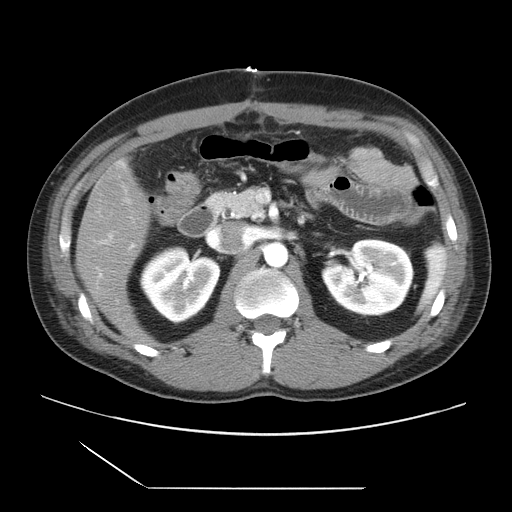
Contrast-enhanced abdominal CT, one axial slice; position 9 of 39 along the scan axis; intravenous contrast given; soft-tissue window (W 400 / L 40 HU); 5 mm slice thickness; 512 × 512 image matrix, field of view 395 × 395 mm. Male patient, age 39 years. From the clinical record (not read from this slice): diagnosis: colorectal cancer liver metastases, imaged before liver resection; multiple liver metastases: yes; largest metastasis: 1.3 cm.
Structures marked on this image (outlined manually by an expert reader):
- hepatic veins: bounding box [x1, y1, x2, y2] px = [213, 228, 247, 249]
- liver: [78, 162, 152, 345]
- portal vein (with intrahepatic branches): [98, 234, 135, 278]